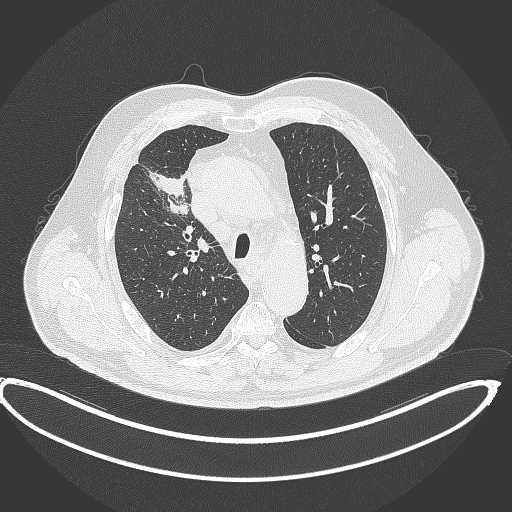
Chest CT, one axial slice. Slice 294 of 390 in the series (ordered by position). Lung window (W 1500 / L -600 HU). 1 mm slice thickness. 512 × 512 image matrix, field of view 448 × 448 mm. Male patient, age 62 years. From the clinical record (not read from this slice): clinical TNM (as recorded): T1c N3 M1c.
Outlined on this slice (rectangle marked by the reading radiologist):
- lung tumour (recorded histology: adenocarcinoma): box from (x=151, y=169) to (x=191, y=219) px